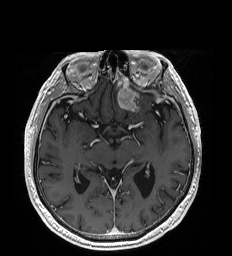
Brain MRI from a brain-tumour surgery series, one axial slice; slice 112 of 192 in the series (ordered by position); T1-weighted post-contrast; 232 × 256 image matrix, field of view 227 × 250 mm. From the clinical record (not read from this slice): histopathology: Glioblastoma; WHO grade: 4; IDH mutation: no.
Annotated regions visible in this slice (manually delineated by an expert):
- tumour: box from (x=117, y=88) to (x=138, y=111) px